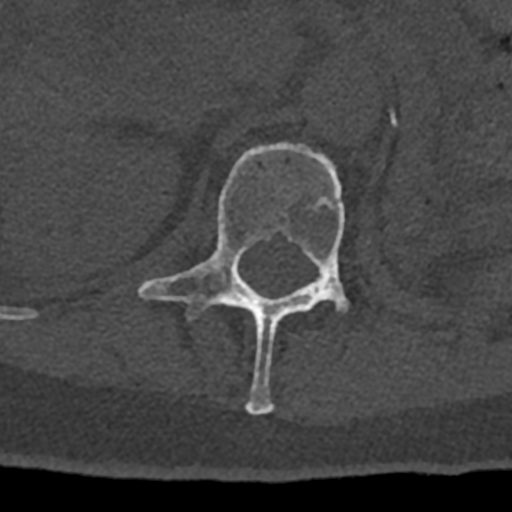
CT including the spine, one axial slice. Slice 435 of 797 in the series (ordered by position). Reconstruction kernel Br40s/3. 120 kVp. Bone window (W 1800 / L 400 HU). 512 × 512 image matrix. Patient: male, 74 years. Case-level facts recorded for this patient, not image findings: primary cancer: renal.
Outlined on this slice (semi-automatic segmentation, software-assisted and operator-edited):
- L1 vertebra: box from (x=138, y=142) to (x=350, y=415) px